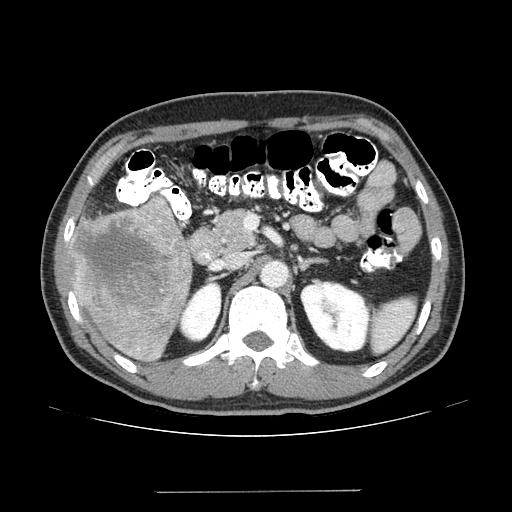
Contrast-enhanced abdominal CT (liver protocol), one axial slice; slice 71 of 131 in the series (ordered by position); reconstruction kernel STANDARD; 100 kVp; one of 2 acquisitions stored at this slice position; soft-tissue window (W 400 / L 40 HU); 2.5 mm slice thickness; 512 × 512 image matrix, field of view 380 × 380 mm. Case-level facts recorded for this patient, not image findings: diagnosis: hepatocellular carcinoma (patient treated with transarterial chemoembolisation; whether this scan precedes or follows treatment is not stated here); TNM stage (as recorded): Stage-I; Child-Pugh class: A.
Annotated regions visible in this slice (semi-automatic segmentation, software-assisted and operator-edited):
- liver parenchyma outside the tumour (the mass and vessels are separate outlines, so this box may not span the whole liver): box from (x=71, y=210) to (x=192, y=362) px
- mass: (x=72, y=195)–(x=191, y=326)